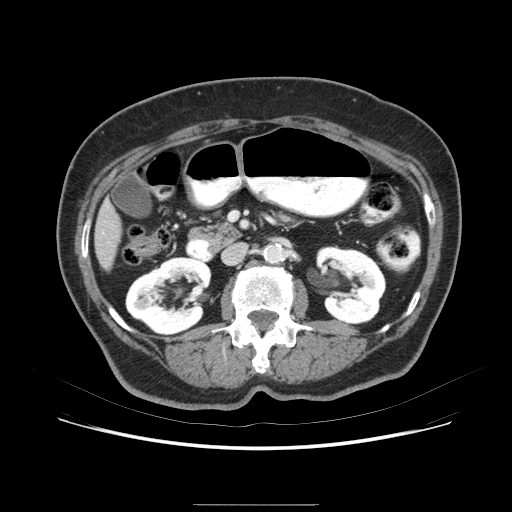
Contrast-enhanced abdominal CT (liver protocol), one axial slice; 120 kVp; soft-tissue window (W 400 / L 40 HU); 512 × 512 image matrix, field of view 380 × 380 mm. Case-level facts recorded for this patient, not image findings: diagnosis: hepatocellular carcinoma (patient treated with transarterial chemoembolisation; whether this scan precedes or follows treatment is not stated here); TNM stage (as recorded): Stage-I; Child-Pugh class: A; tumour differentiation: poorly differentiated; tumour nodularity: uninodular.
Structures marked on this image (semi-automatically segmented with operator editing):
- liver parenchyma outside the tumour (the mass and vessels are separate outlines, so this box may not span the whole liver): bounding box <92,136,248,290> (left, top, right, bottom; pixels)
- liver vessels: <110,234,113,238>